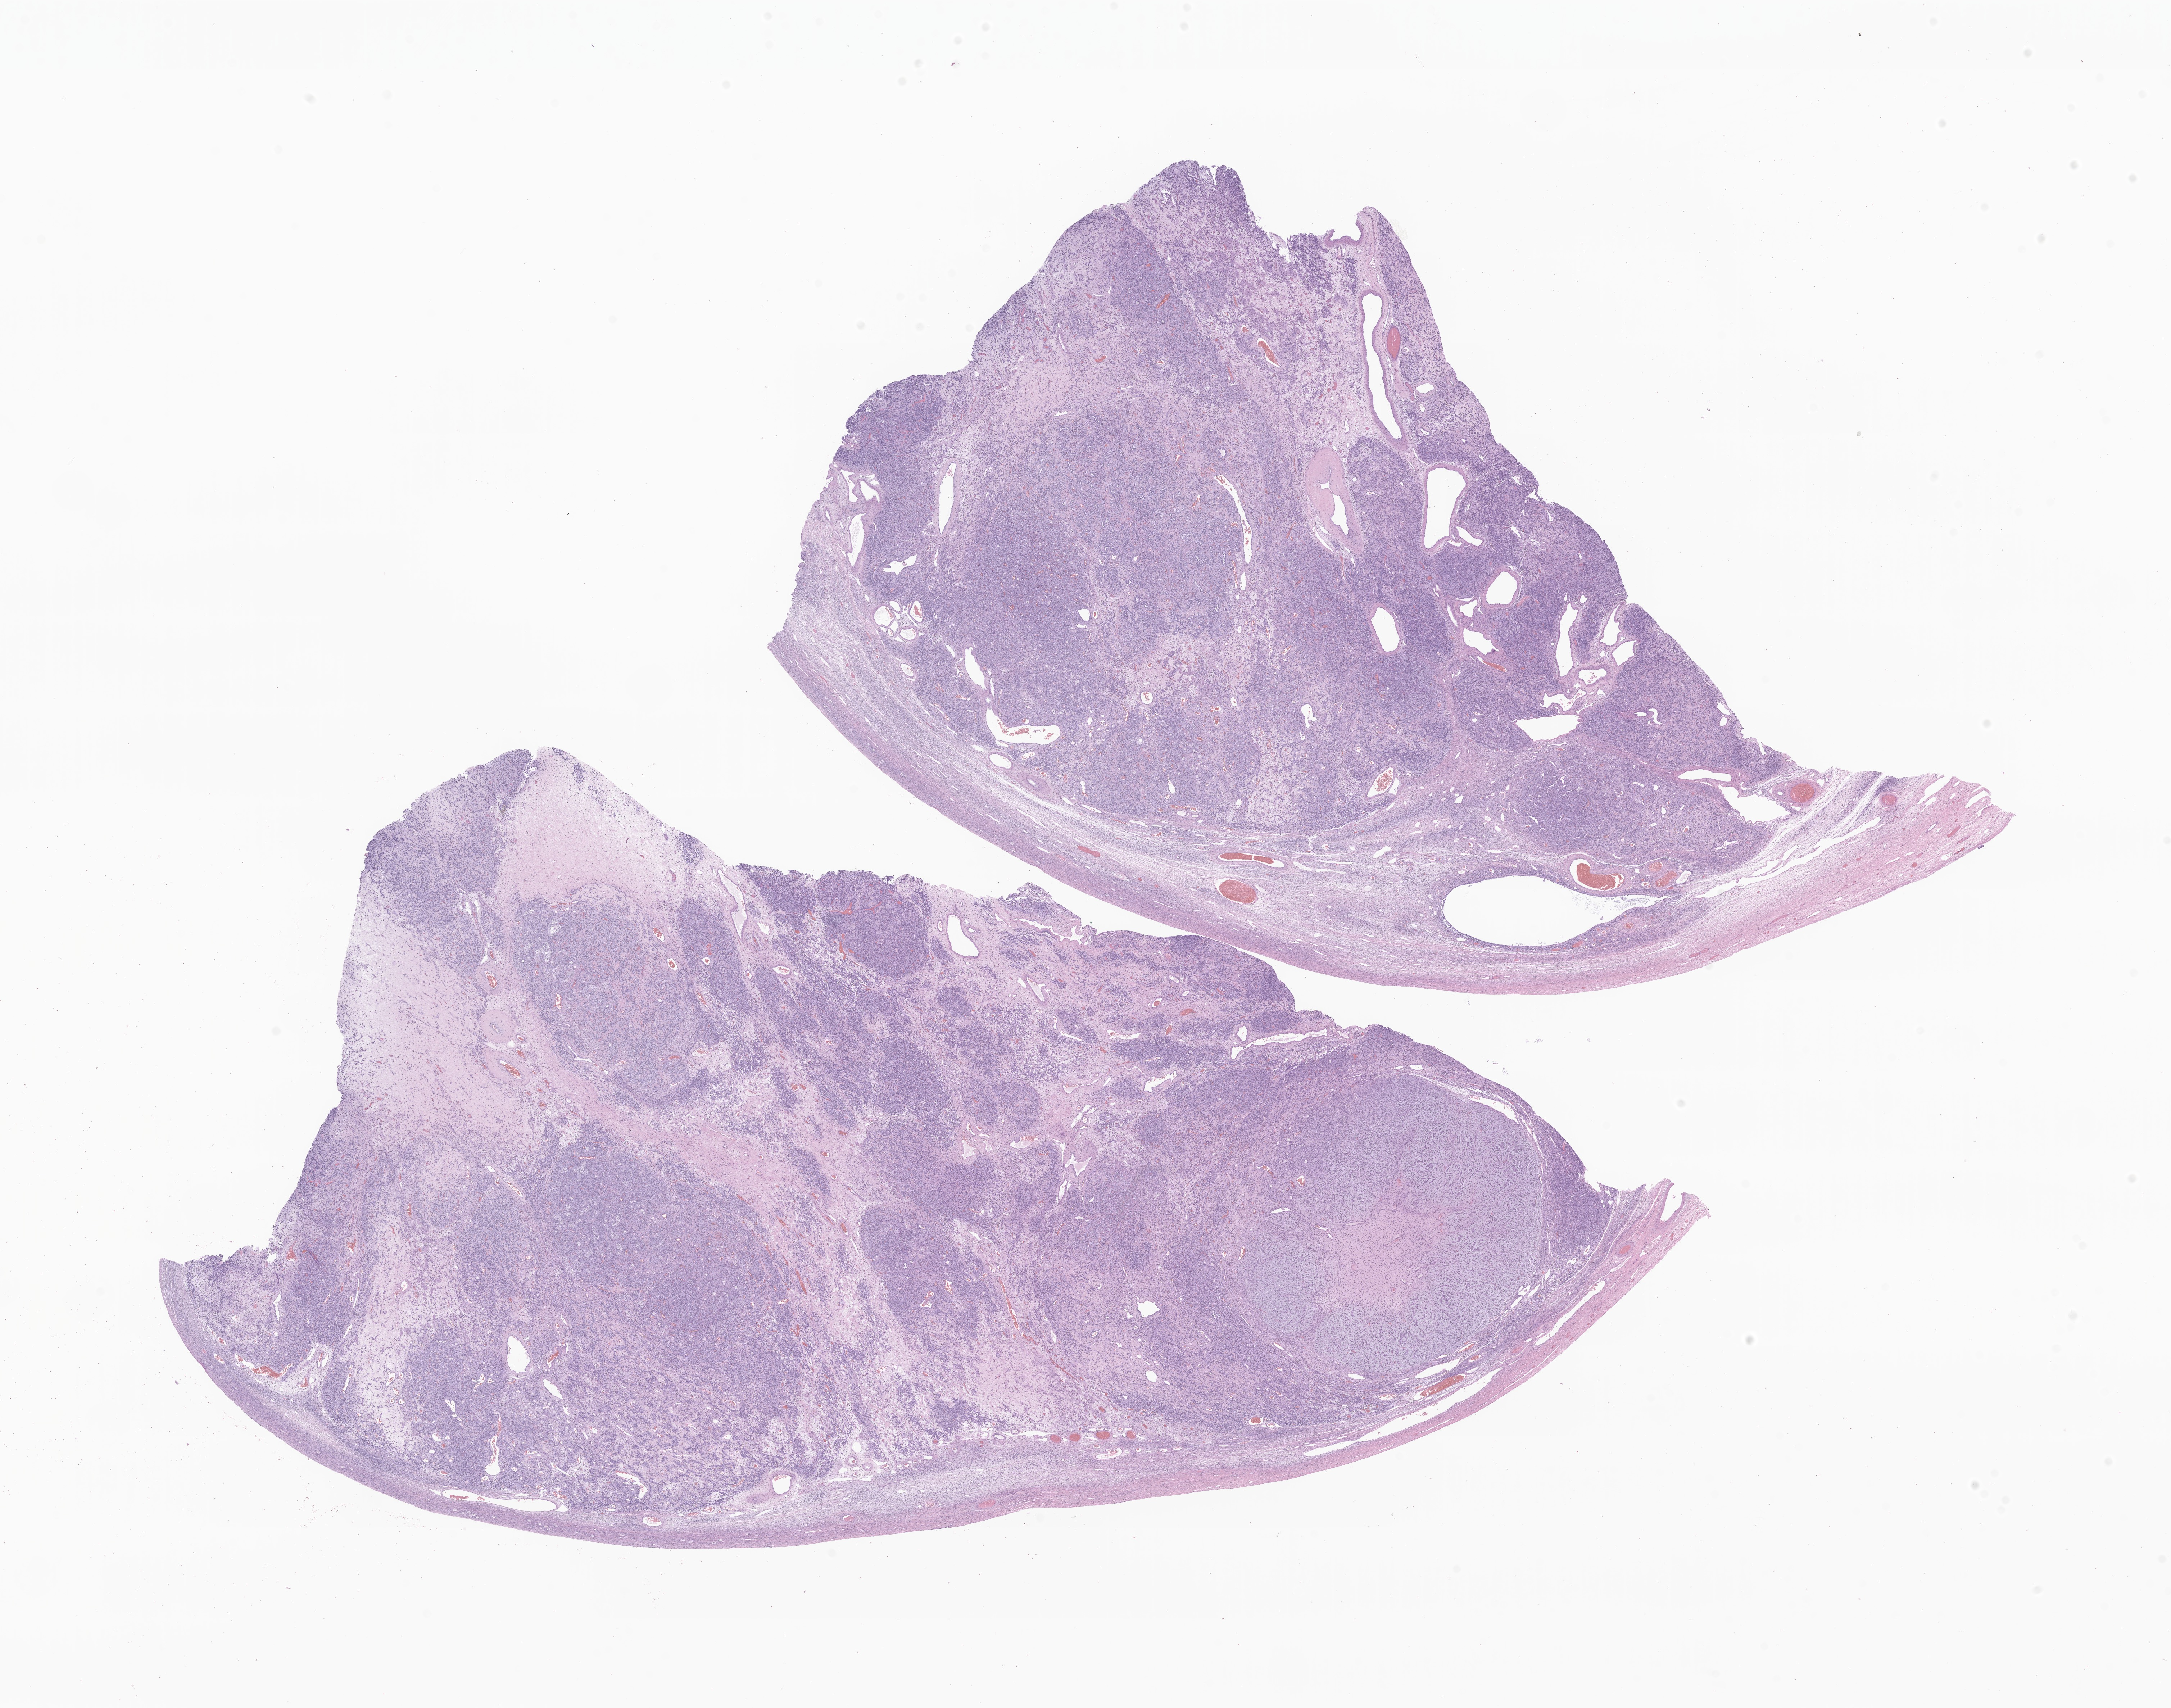
Whole-slide image, haematoxylin and eosin stain of tumor tissue from the ovary, low-resolution overview of the scanned area, about 25.4 x 20.0 mm. FFPE section. Patient: female, age 179 months.
Diagnosis (ICD-O-3 morphology term): Sex cord-gonadal stromal tumor, incompletely differentiated.